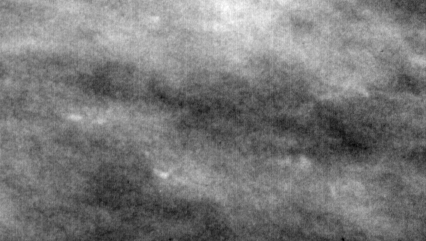
Region of interest cut from a scanned film mammogram (one marked finding), right breast, MLO view.
- Marked abnormality: calcifications, morphology pleomorphic, distribution linear; BI-RADS assessment category 4; pathology result (as recorded, not read from the image): malignant.